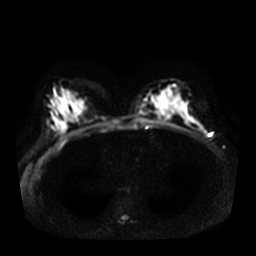
Breast MRI, one axial slice. Position 16 of 30 along the scan axis. Diffusion-weighted series; image 2 of 4 stored at this slice position (different b-values; order by instance number). 3 T. 5 mm slice thickness. 256 × 256 image matrix. Female patient.
Structures marked on this image (expert manual segmentation):
- tumour on diffusion-weighted imaging: box from (x=205, y=133) to (x=207, y=136) px